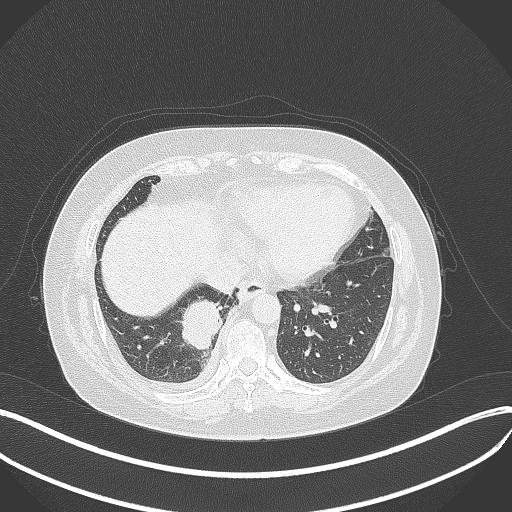
Chest CT, one axial slice; position 108 of 381 along the scan axis; 120 kVp; lung window (W 1500 / L -600 HU); 1 mm slice thickness; 512 × 512 image matrix. Patient: female, 56 years. From the clinical record (not read from this slice): clinical TNM (as recorded): T2b N1 M0; histopathological grade: G3.
Outlined on this slice (bounding box drawn by a radiologist):
- lung tumour (recorded histology: small cell carcinoma): bounding box [x1, y1, x2, y2] px = [175, 294, 223, 351]